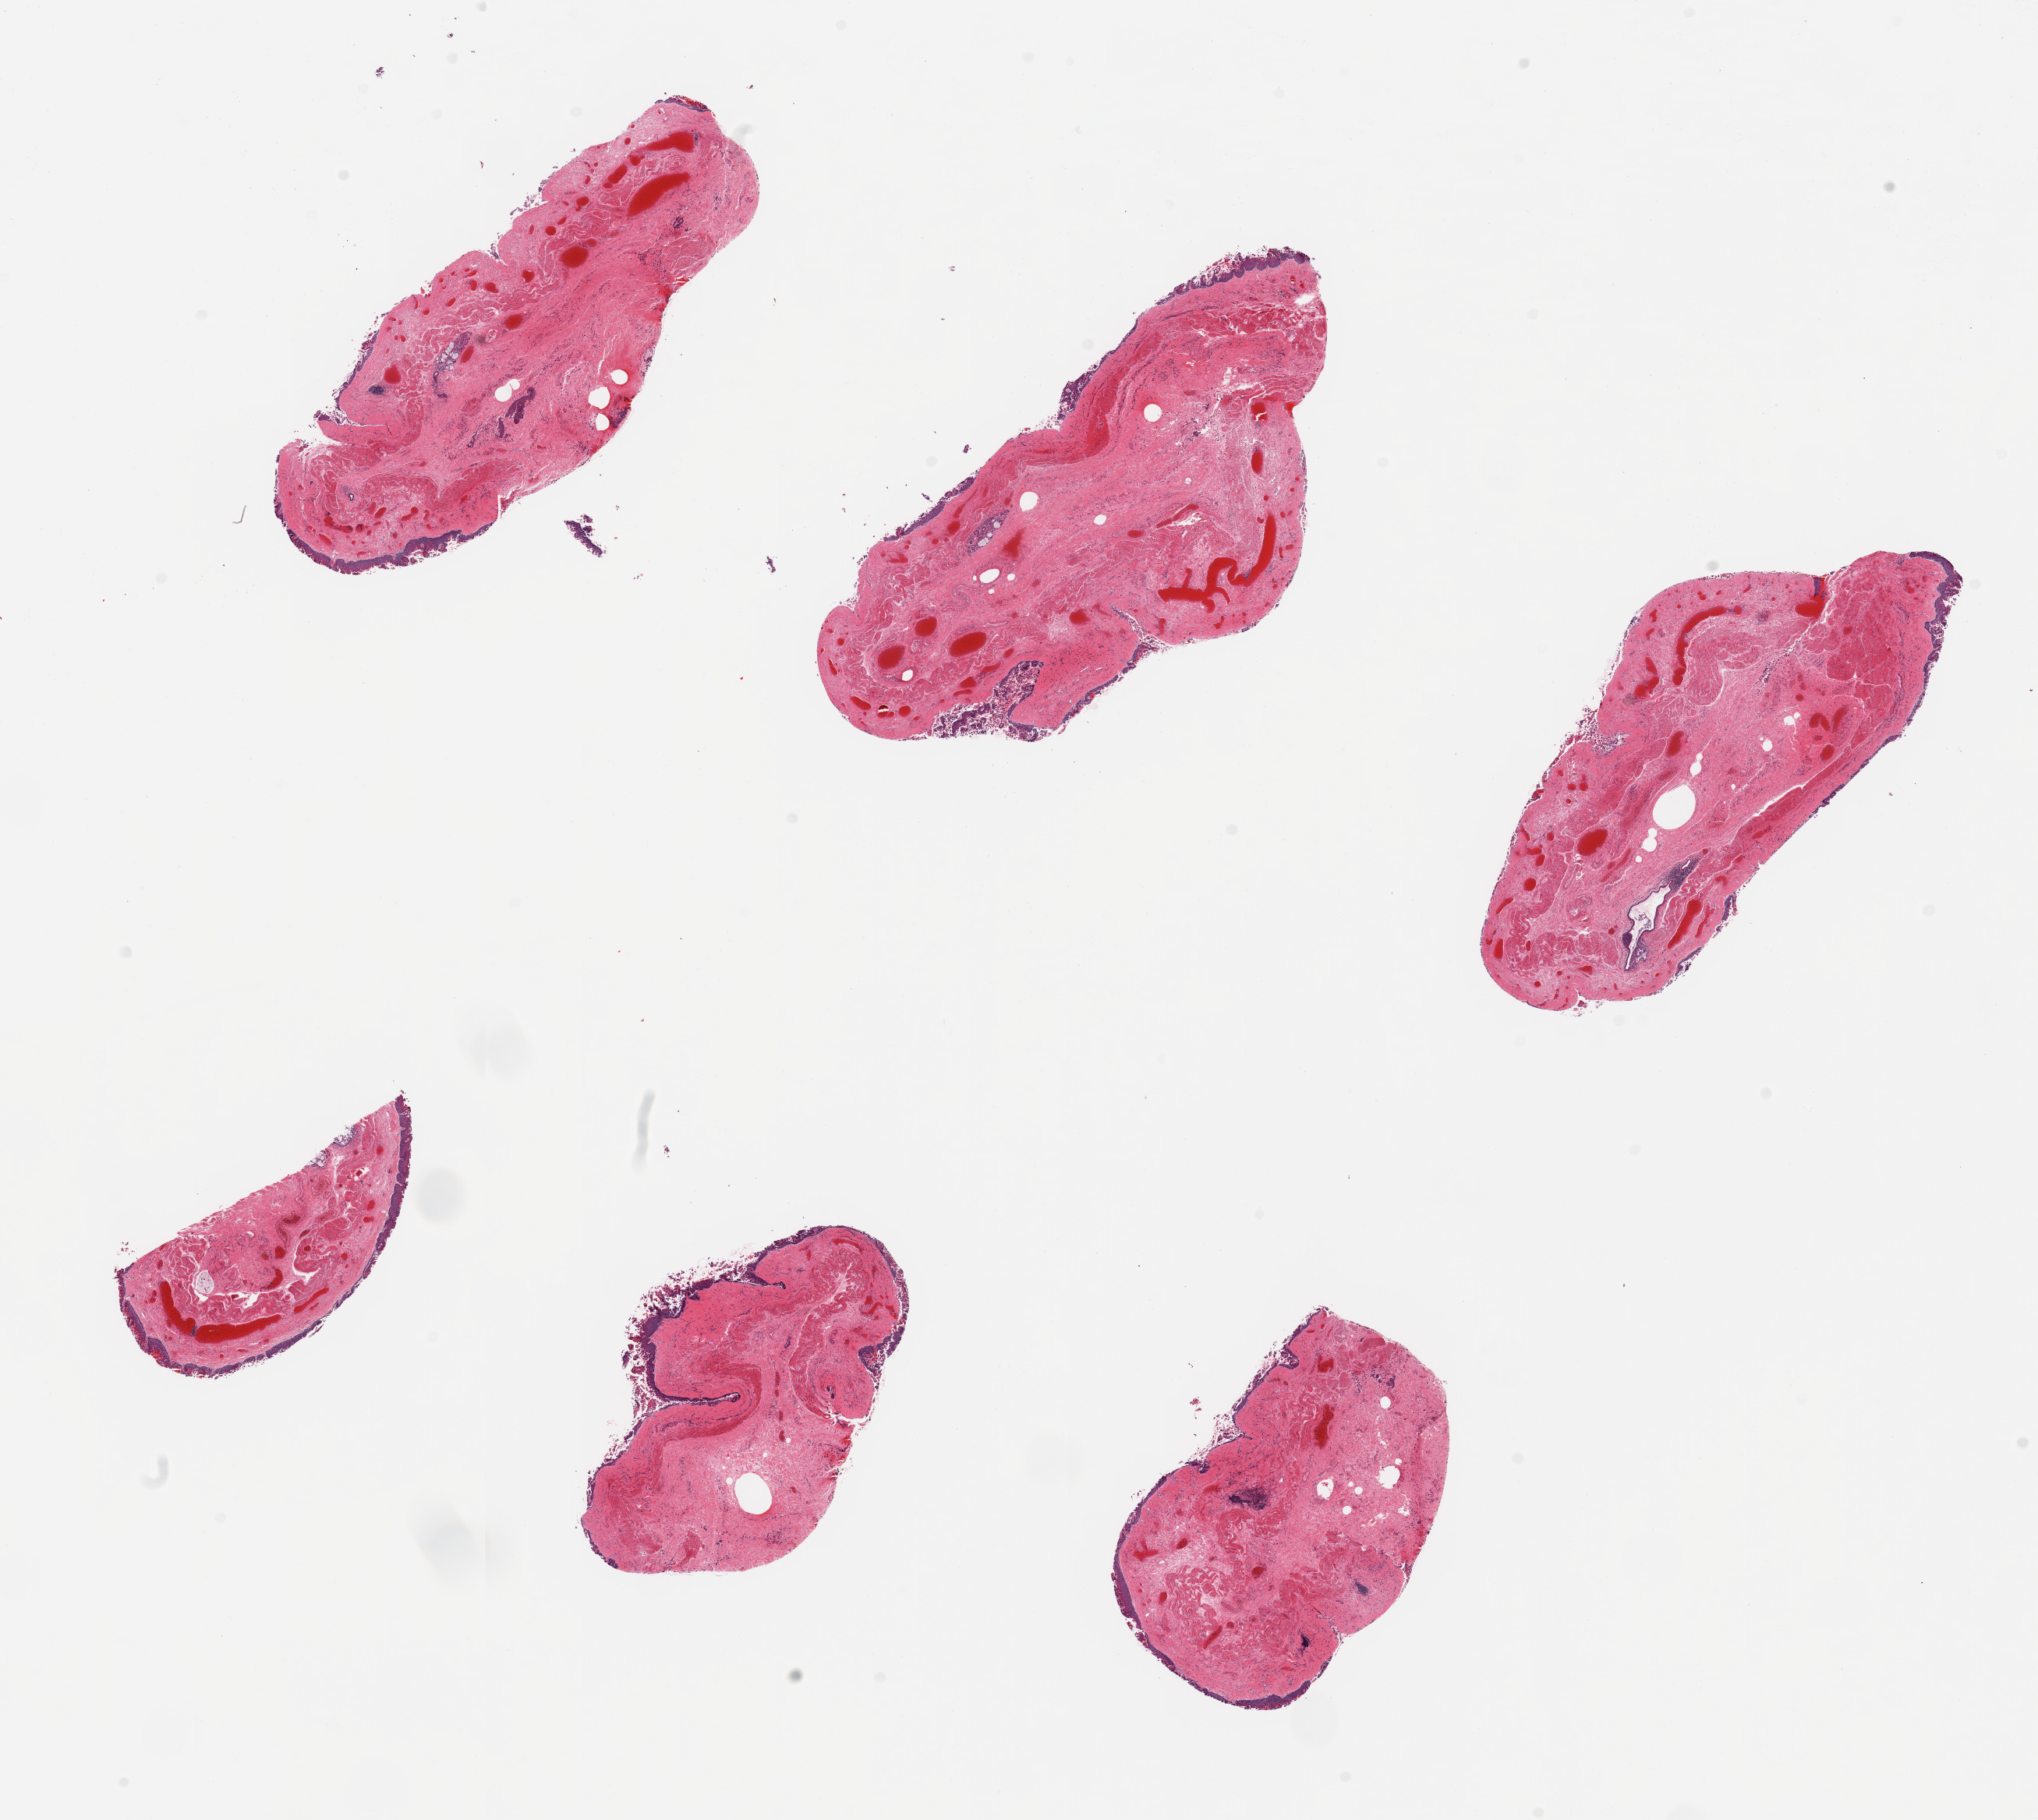
Whole-slide image, haematoxylin and eosin stain, shown as a low-resolution overview of the whole scanned area (about 20.7 x 18.5 mm, acquisition: 20x scan); PAXgene-fixed, paraffin-embedded tissue; target tissue: esophageal mucous membrane; tissue donor sample. Male donor.
Review note (as recorded): 6 pieces, squamous mucosa unusually significantly autolyzed, residucal foci are ~0.1mm, largely sloughed.